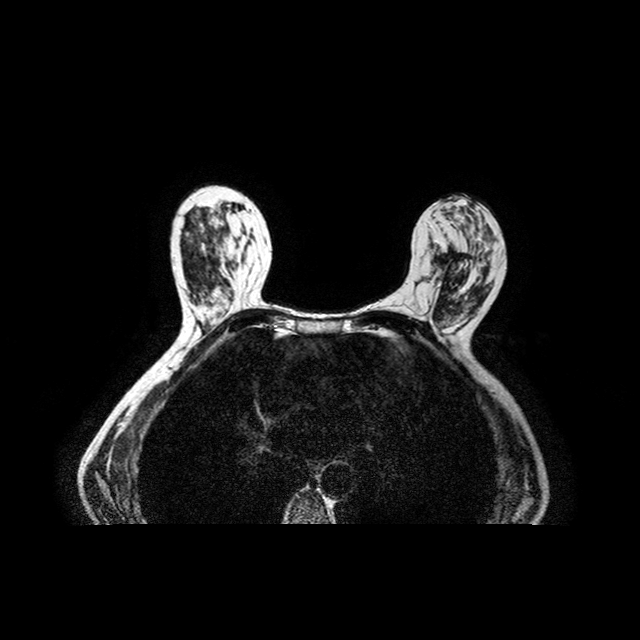
Breast MRI examination; 2 images, each one mid-volume slice chosen by position. Patient in her 50s.
Image 1: axial T2-weighted / STIR image, series "T2W_TSE SENSE", slice 43 of 84.
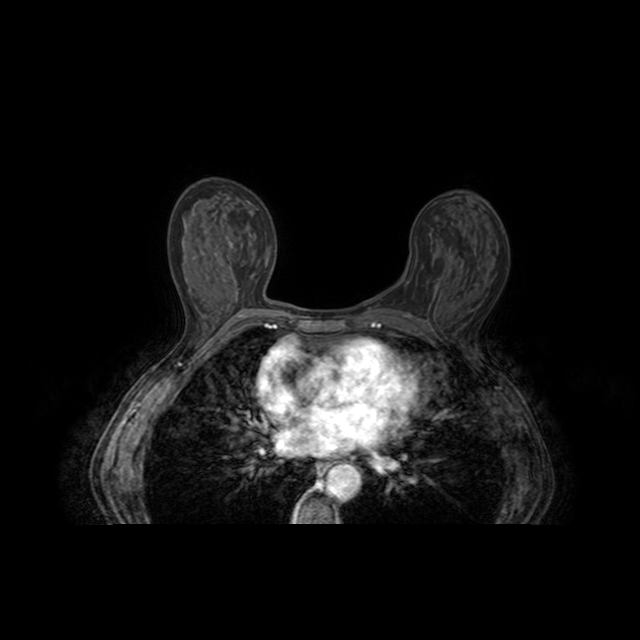
Image 2: post-contrast dynamic axial slice, slice 43 of 84, dynamic phase 5 of 8, 4 mm slice thickness.
Radiologist's MRI impression: 1) 1 cm mass at the 11:00 position in the left breast with suspicious enhancment adjacent to a surgical clip at site of biopsy proven invasive ductal carcinoma. 2) Second surgical clip in the upper, inner quadrant of the right breast at the area of a second site of invasive ductal carcinoma. There is only a minimal residual amount of progressive enhancement surrounding the clip. 3) No suspicious appearing lymph nodes in either axilla. 4) No evidence of malignancy in the right breast; BI-RADS 6.
Patient-level pathology facts (from the clinical record, not from the images): pathology diagnosis: Ductal carcinoma in-situ , solid type, nuclear grade III/III; receptor status (as recorded): ER pos, PR neg, HER2 pos; Ki-67 (as recorded): low prolif.